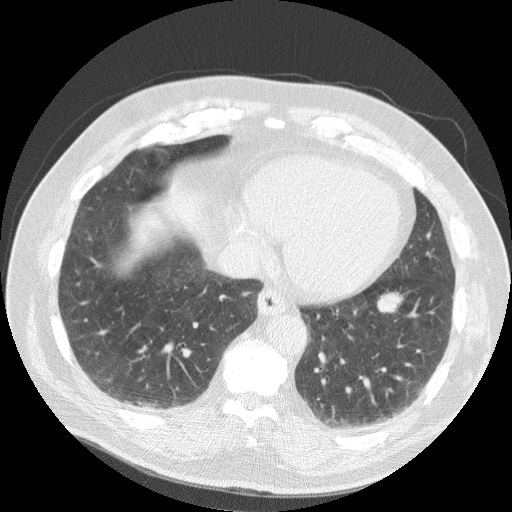
Axial slice from a low-dose chest CT screening exam. Second annual screen. Lung window (W 1500 / L -600 HU). Standard (soft-tissue) reconstruction kernel (STANDARD). 120 kVp. Male participant, aged 63 years at enrolment. Current smoker at enrolment.
• Expert-annotated lung lesion, bounding box (x1, y1, x2, y2) in pixels: (362, 286, 410, 325).
• The screening reader recorded 2 non-calcified nodules or masses ≥4 mm on this exam (right middle lobe, left lower lobe); which of them this box marks is not recorded.
• Later outcome: lung cancer diagnosed 633 days after this screen — squamous cell carcinoma, NOS, left lower lobe, stage IB (AJCC 6th edition), 48 mm at pathology.